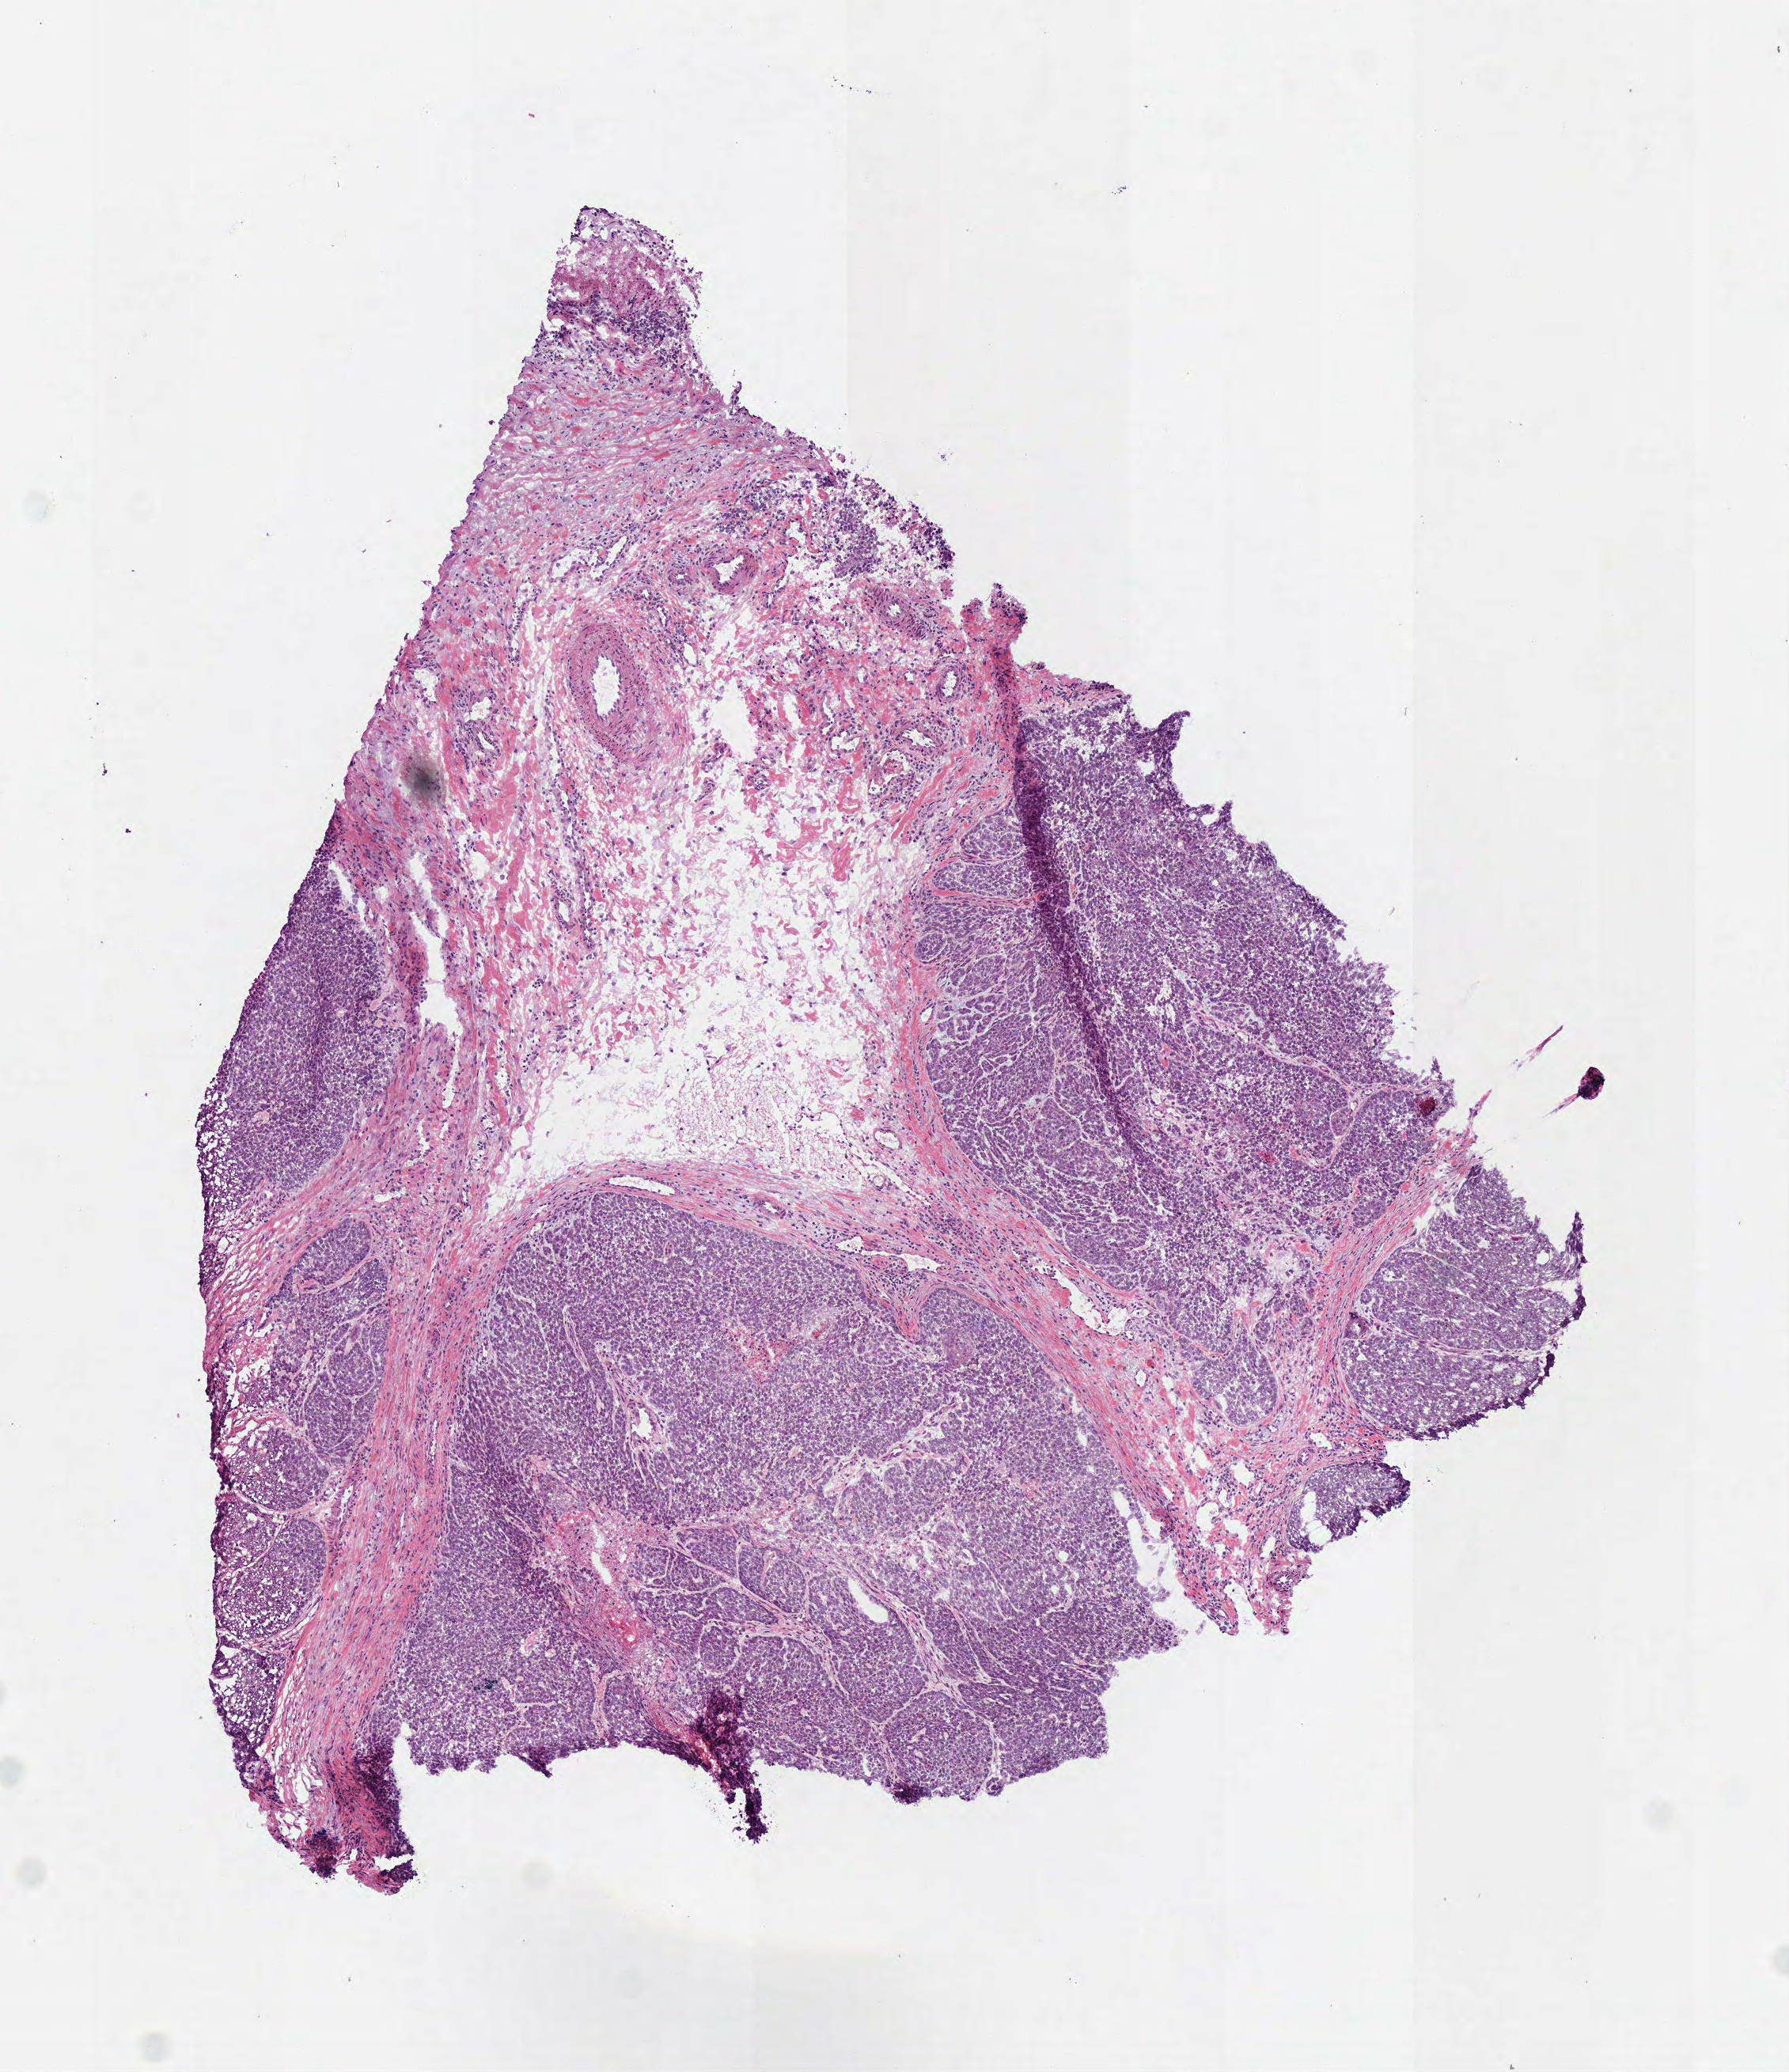
Whole-slide histology image, H&E-stained, shown as a low-resolution overview of the whole scanned area (about 4.5 x 5.2 mm, from a 40x scan); frozen section from the bottom of the tissue portion; primary tumour sample from the head and neck. Female, age 55 years at initial diagnosis. Histologic grade: G3 (poorly differentiated). Composition of this section per pathologist review: tumour cells 69%, tumour nuclei 80%, normal cells 0%, stromal cells 30%, necrosis 1%.
Histologic diagnosis: Squamous cell carcinoma, NOS (lip, NOS). AJCC pathologic stage: I (7th edition). TNM: T1 N0. Laterality: right.